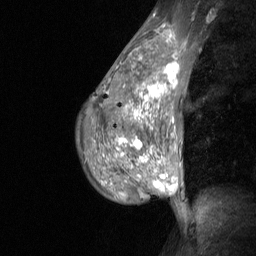
Breast MRI (dynamic contrast-enhanced), one sagittal slice; dynamic contrast-enhanced study with each time point stored as its own series, time point 2 of 3 at this slice position (early post-contrast, ordered by acquisition time); 1.5 T; TE 4.8 ms, TR 27 ms; 256 × 256 image matrix. Patient: female, 36 years. From the clinical record (not read from this slice): setting: breast cancer imaged before/during neoadjuvant chemotherapy; receptor status: HR-positive, HER2-negative.
Annotated regions visible in this slice (semi-automatic segmentation, software-assisted and operator-edited):
- analysis volume of interest (the breast-tissue region the enhancement analysis was run in; not a lesion): bounding box <77,45,187,210> (left, top, right, bottom; pixels)
- tumour enhancement mask (voxels above the 90 % enhancement threshold inside the analysis volume of interest): <116,62,179,190>